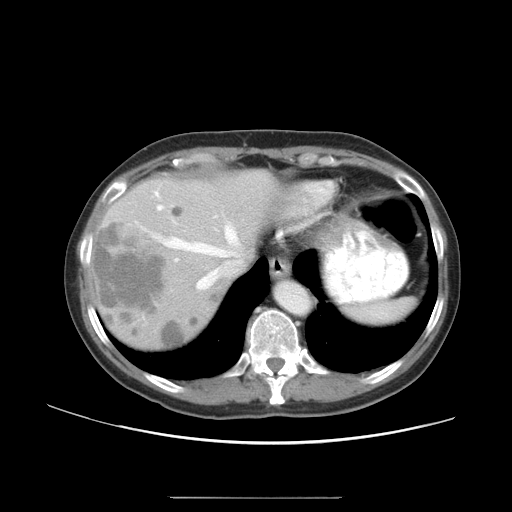
Contrast-enhanced abdominal CT, one axial slice. Position 39 of 50 along the scan axis. Intravenous contrast given. Soft-tissue window (W 400 / L 40 HU). 5 mm slice thickness. 512 × 512 image matrix, field of view 389 × 389 mm. Female patient, age 58 years. Case-level facts recorded for this patient, not image findings: diagnosis: colorectal cancer liver metastases, imaged before liver resection.
Outlined on this slice (outlined manually by an expert reader):
- hepatic veins: box from (x=154, y=190) to (x=239, y=290) px
- liver: (x=94, y=173)–(x=275, y=345)
- planned liver remnant (the part of the liver to remain after resection): (x=191, y=173)–(x=275, y=249)
- portal vein (with intrahepatic branches): (x=156, y=205)–(x=165, y=211)
- liver metastasis: (x=162, y=320)–(x=186, y=349)
- liver metastasis: (x=173, y=206)–(x=183, y=219)
- liver metastasis: (x=212, y=296)–(x=220, y=307)
- liver metastasis: (x=96, y=220)–(x=164, y=324)